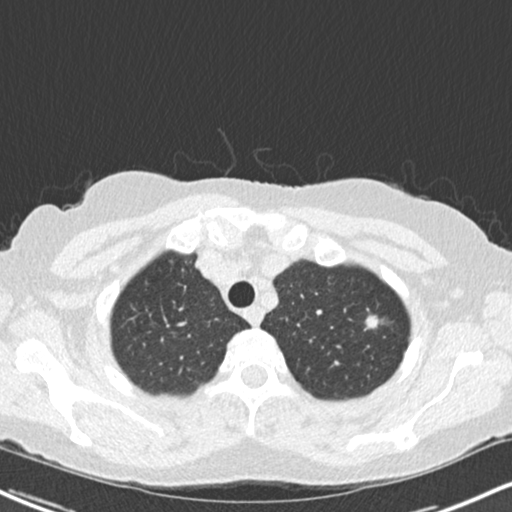
Low-dose screening chest CT, axial slice. First (baseline) screen. Lung window (W 1500 / L -600 HU). Standard (soft-tissue) reconstruction kernel (B30f). Slice 25 of 217 in the series. 512 × 512 image matrix. Female, age 64 years at enrolment.
Expert reader's lesion annotation, bounding box (x1, y1, x2, y2) in pixels: (358, 307, 389, 339). The screening reader recorded 2 non-calcified nodules or masses ≥4 mm on this exam (left upper lobe, lingula); which of them this box marks is not recorded.